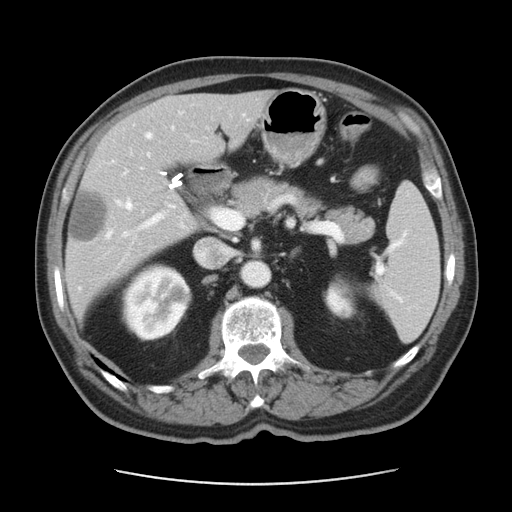
Contrast-enhanced abdominal CT, one axial slice; slice 24 of 42 in the series (ordered by position); reconstruction kernel STANDARD; 120 kVp; soft-tissue window (W 400 / L 40 HU); 512 × 512 image matrix. Male patient, age 73 years. From the clinical record (not read from this slice): diagnosis: colorectal cancer liver metastases, imaged before liver resection; multiple liver metastases: yes; largest metastasis: 0.5 cm; disease in both lobes: no.
Outlined on this slice (outlined manually by an expert reader):
- hepatic veins: bounding box [x1, y1, x2, y2] px = [78, 134, 151, 290]
- liver: [66, 91, 269, 318]
- planned liver remnant (the part of the liver to remain after resection): [111, 91, 269, 198]
- portal vein (with intrahepatic branches): [124, 211, 223, 235]
- liver metastasis: [71, 191, 107, 242]